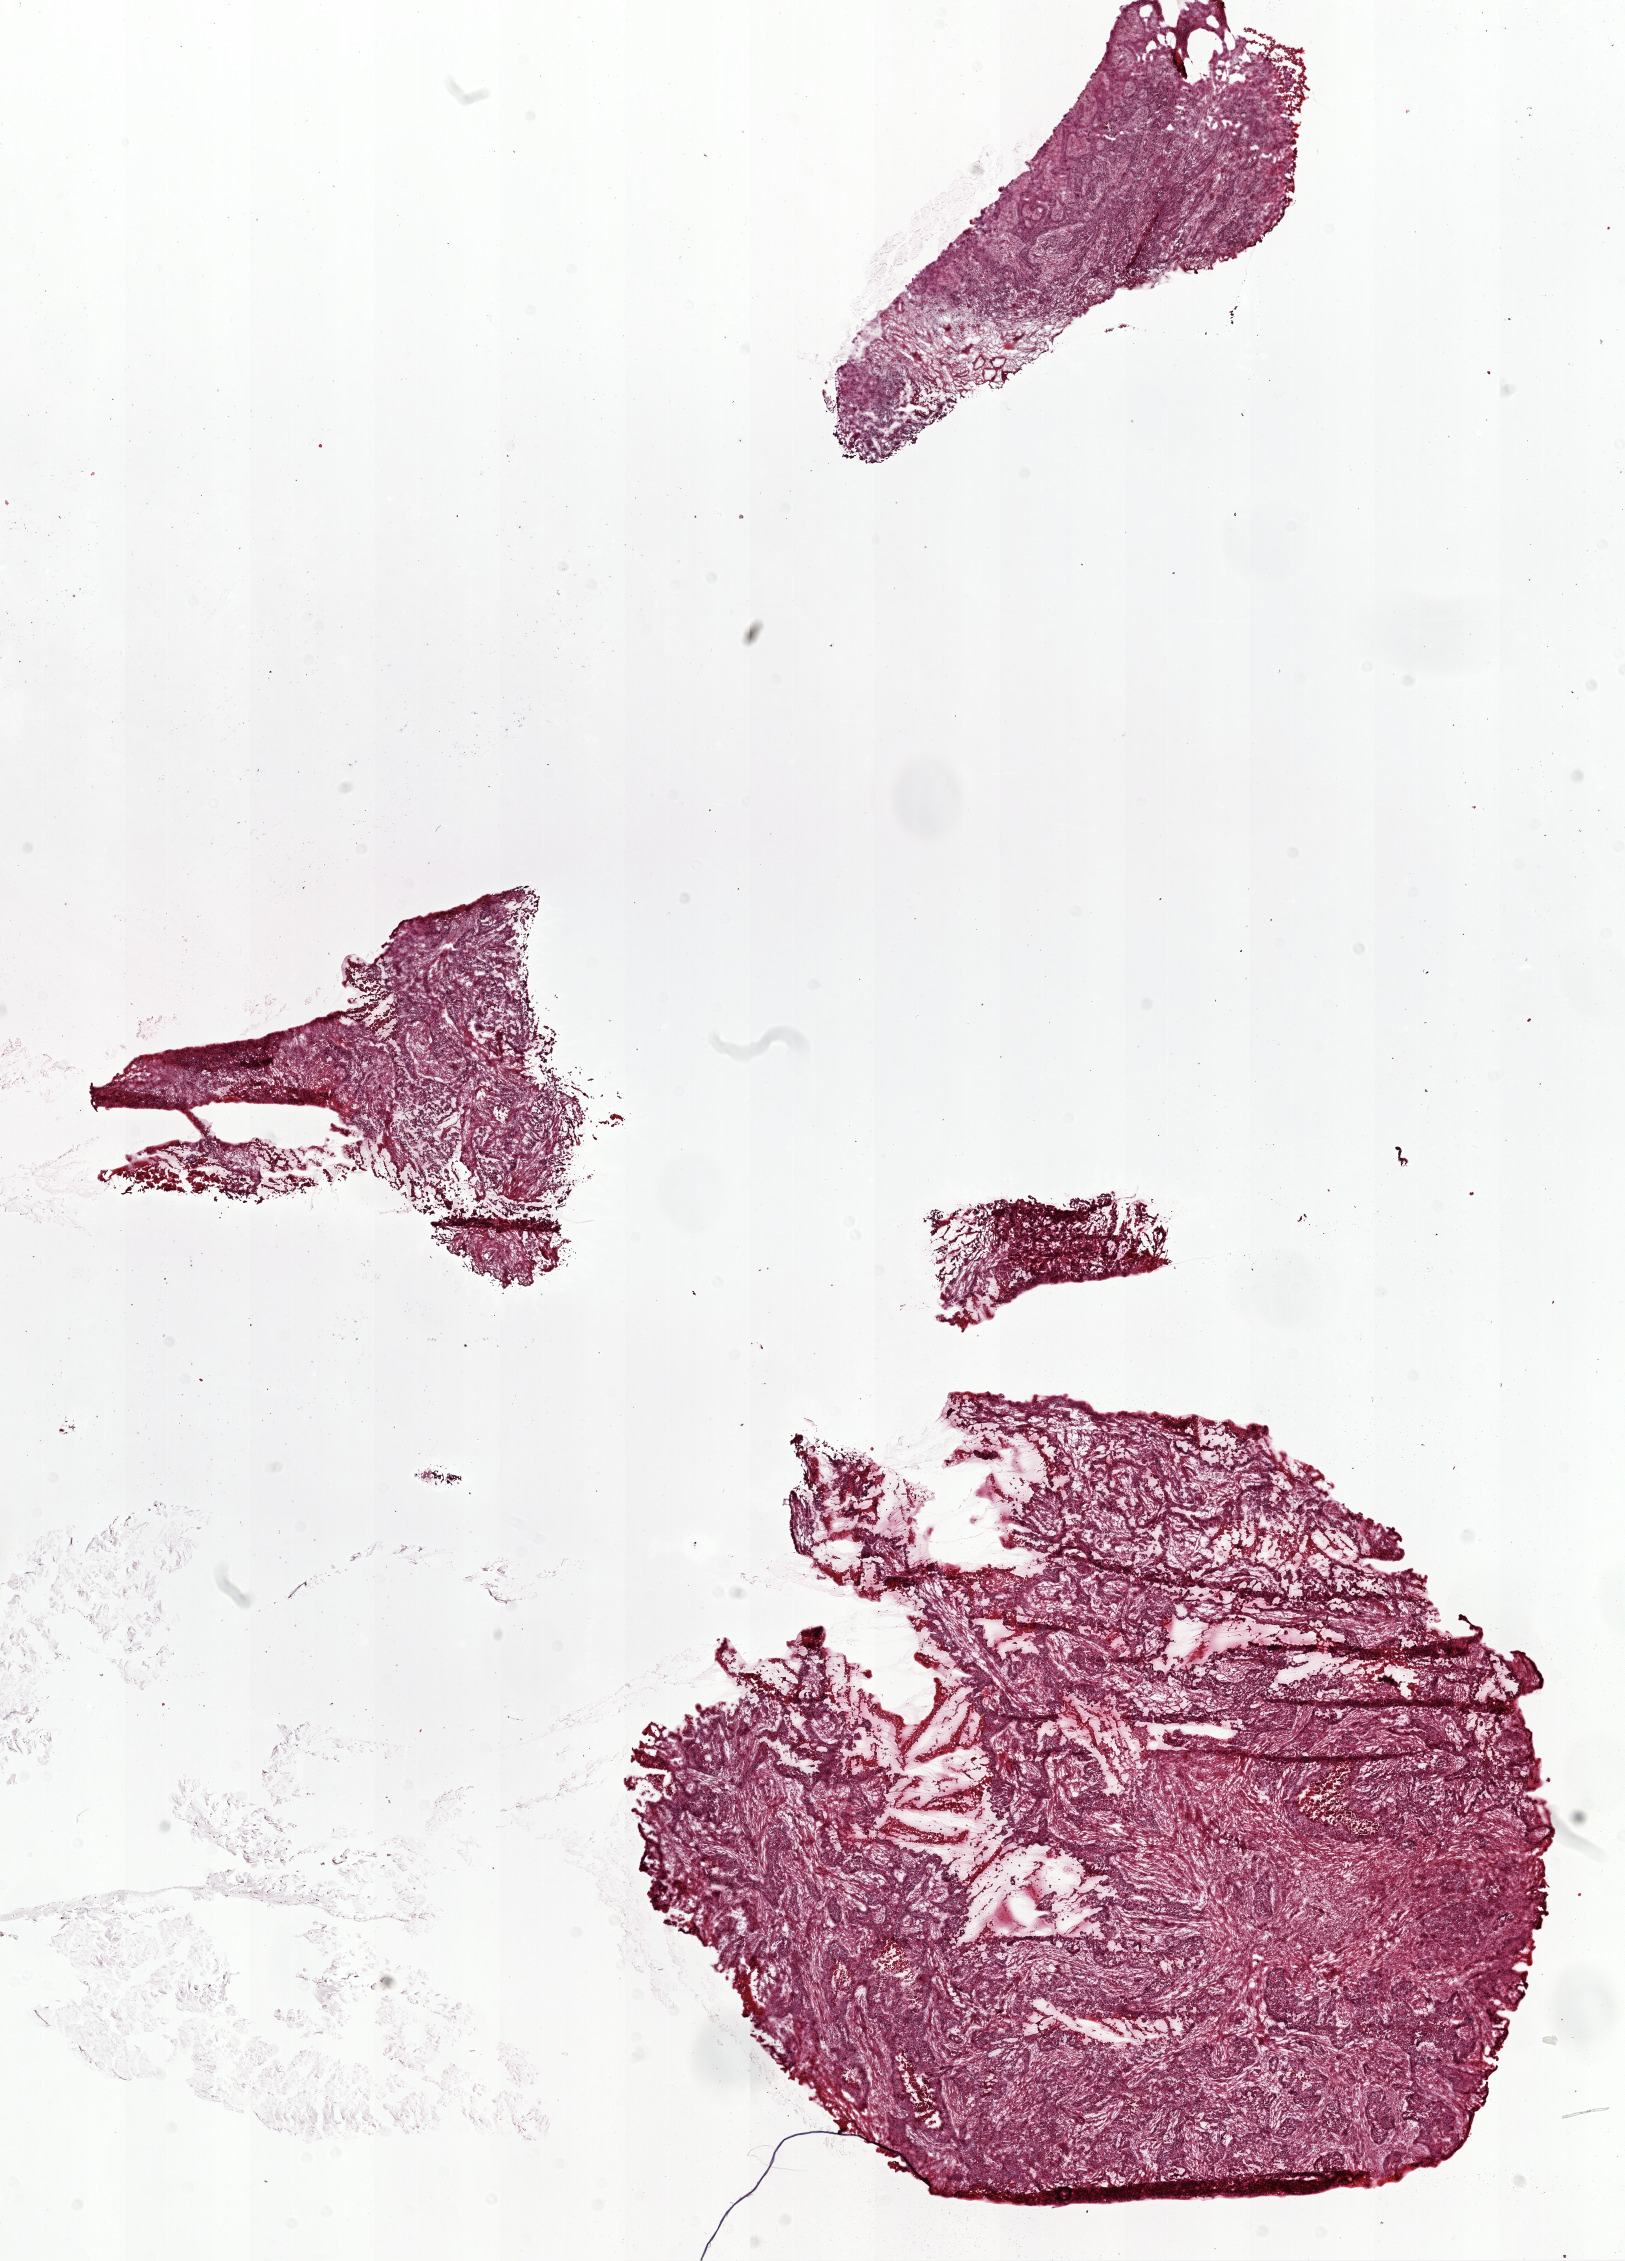
H&E-stained whole-slide image — a low-resolution overview of the entire scanned area, about 13.0 x 18.1 mm (acquisition: 20x scan), frozen section, ovary, primary tumour sample. Female, age 72 years at initial diagnosis. Histologic grade: G3 (poorly differentiated). Composition of this section per pathologist review: tumour cells 80%, tumour nuclei 95%, normal cells 0%, stromal cells 20%, necrosis 0%.
• pathologic diagnosis: Serous cystadenocarcinoma, NOS
• FIGO stage: IIIC
• laterality: bilateral